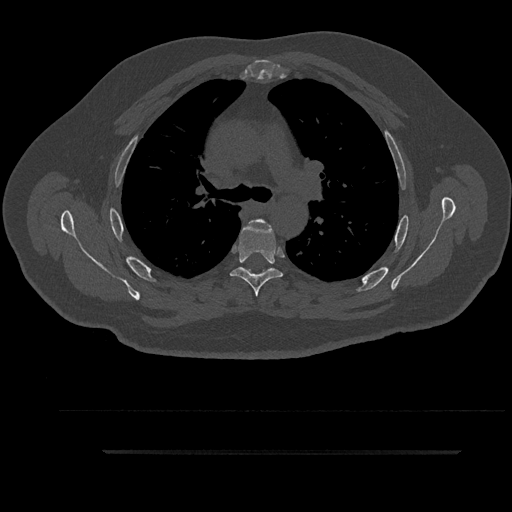
CT including the spine, one axial slice; position 629 of 797 along the scan axis; bone window (W 1800 / L 400 HU); 0.5 mm slice thickness; 512 × 512 image matrix, field of view 432 × 432 mm. Patient: male, 63 years. Case-level facts recorded for this patient, not image findings: primary cancer: renal.
Outlined on this slice (semi-automatically segmented with operator editing):
- T4 vertebra: bounding box <248,219,271,227> (left, top, right, bottom; pixels)
- T5 vertebra: <230,221,283,297>
- T6 vertebra: <244,268,271,275>